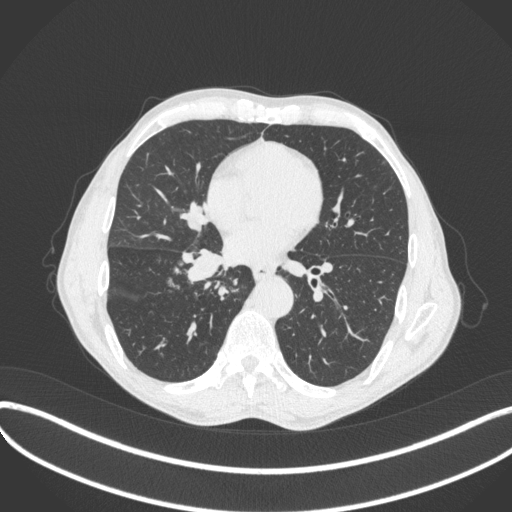
Chest CT, one axial slice; position 194 of 481 along the scan axis; lung window (W 1500 / L -600 HU); 1 mm slice thickness; 512 × 512 image matrix, field of view 400 × 400 mm. Patient: male, 65 years. Case-level facts recorded for this patient, not image findings: clinical TNM (as recorded): T2a N0 M0; histopathological grade: G2.
Outlined on this slice (rectangle marked by the reading radiologist):
- lung tumour (recorded histology: squamous cell carcinoma): box from (x=173, y=243) to (x=227, y=284) px